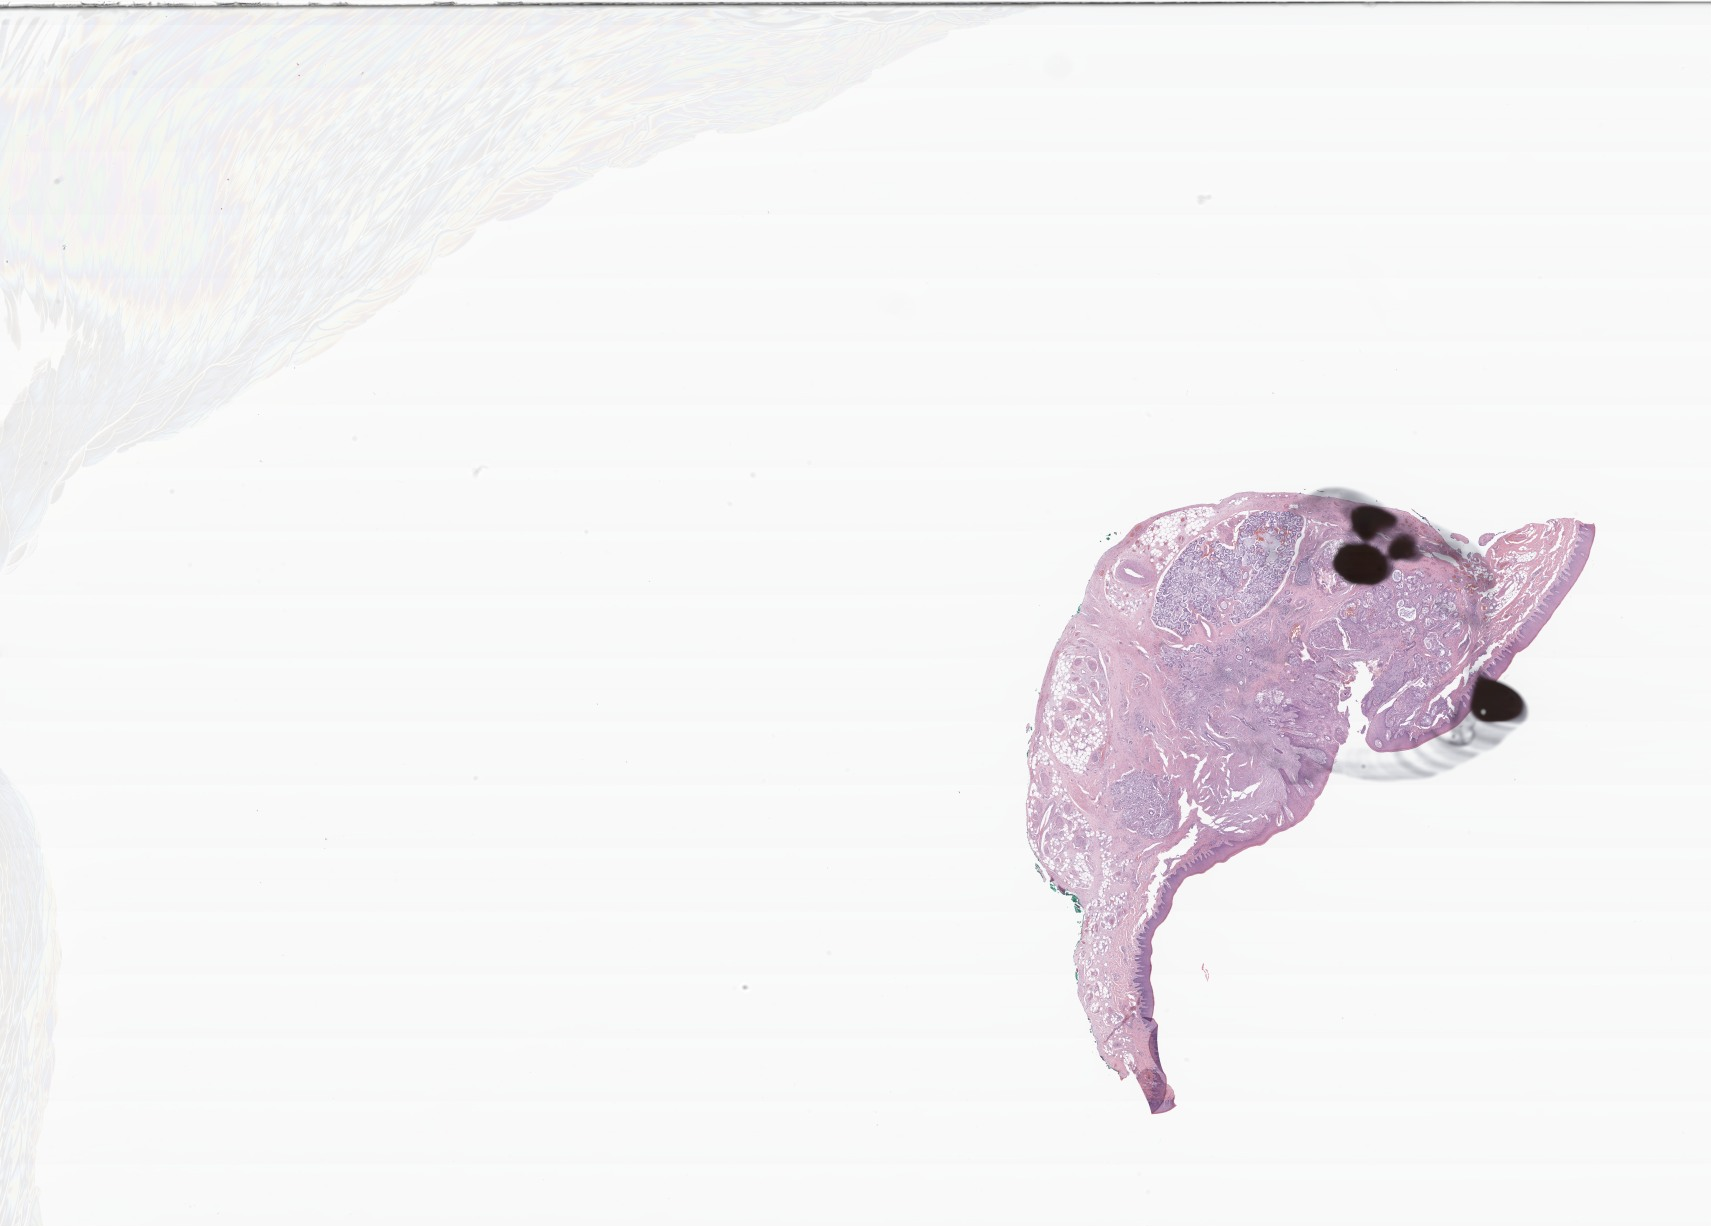
Whole-slide image, haematoxylin and eosin stain of tumor tissue from the hard palate, whole scanned area (about 28.8 x 20.6 mm) shown as a low-resolution overview; FFPE section. Patient female; age 90 months (7 years 6 months).
Recorded diagnosis: Mucoepidermoid carcinoma.